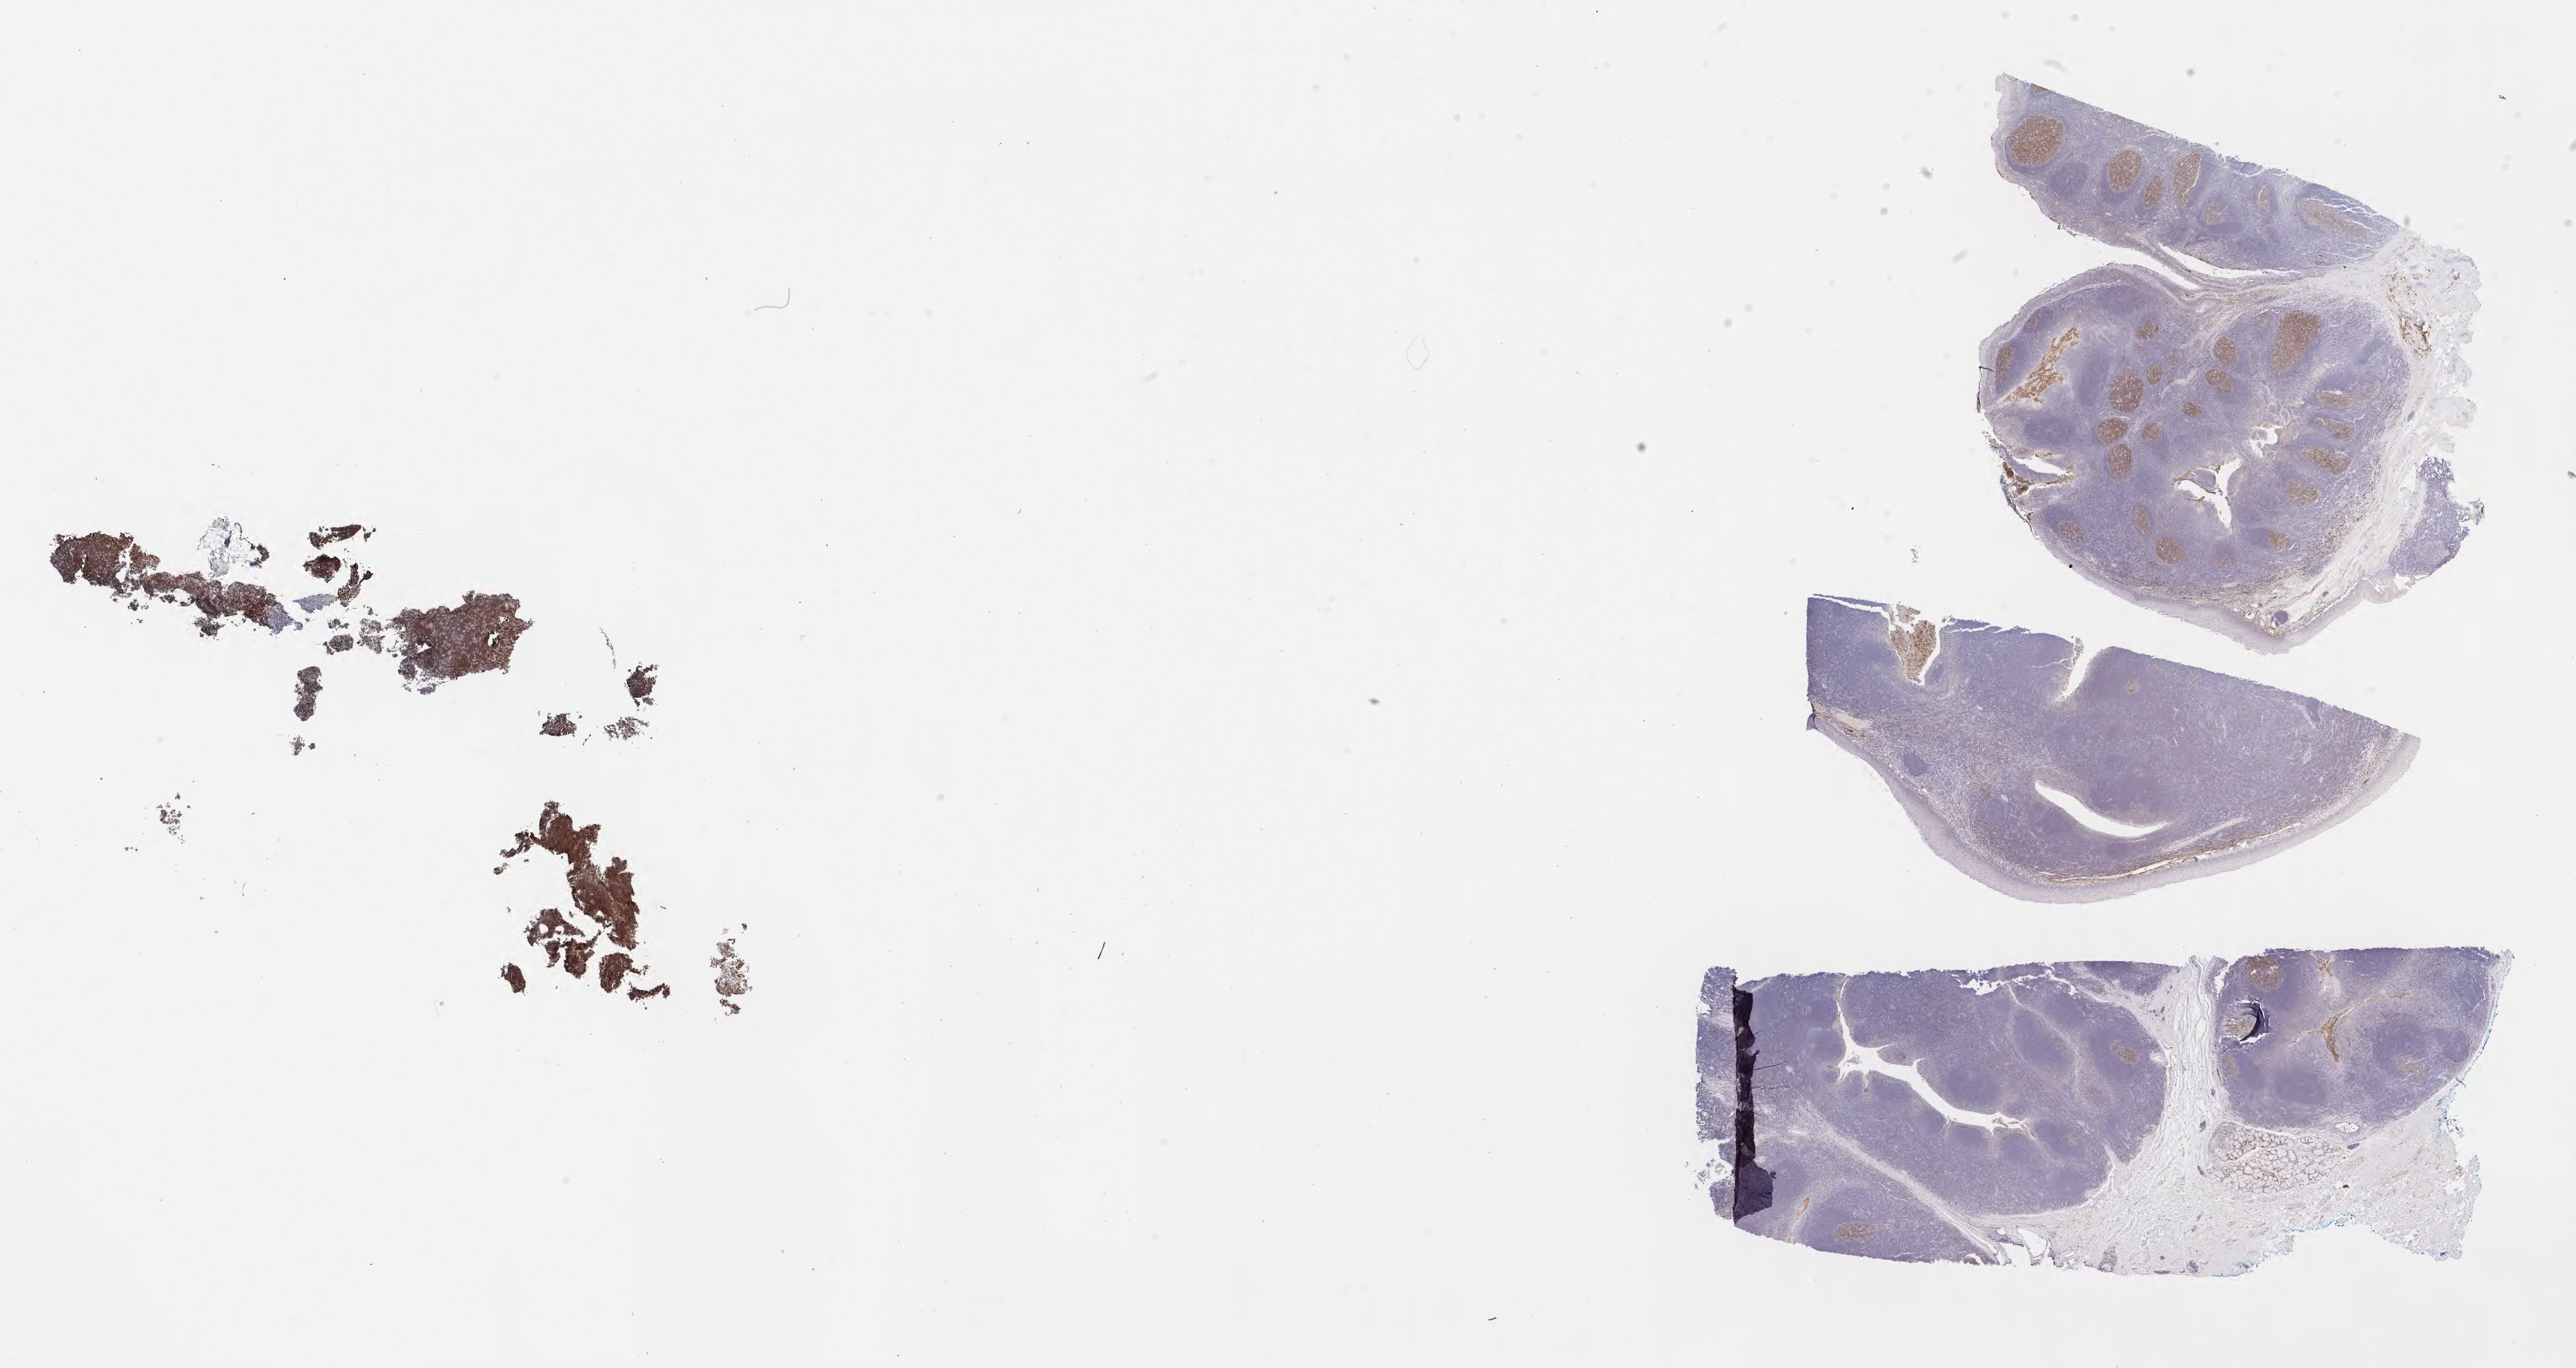
Whole-slide image, immunohistochemical stain for CD10 — whole scanned area (about 30.2 x 16.0 mm) shown as a low-resolution overview, tumor tissue, anatomic site: cranium. Female patient; age at initial diagnosis 1 years.
• histologic diagnosis: Burkitt lymphoma, NOS